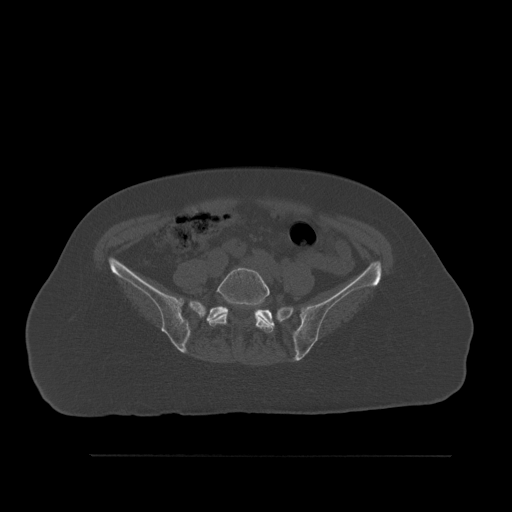
CT including the spine, one axial slice. Position 183 of 527 along the scan axis. Bone window (W 1800 / L 400 HU). 1.5 mm slice thickness. 512 × 512 image matrix. Female patient, age 73 years. From the clinical record (not read from this slice): primary cancer: breast.
Outlined on this slice (semi-automatically segmented with operator editing):
- L5 vertebra: bounding box [x1, y1, x2, y2] px = [206, 267, 274, 333]